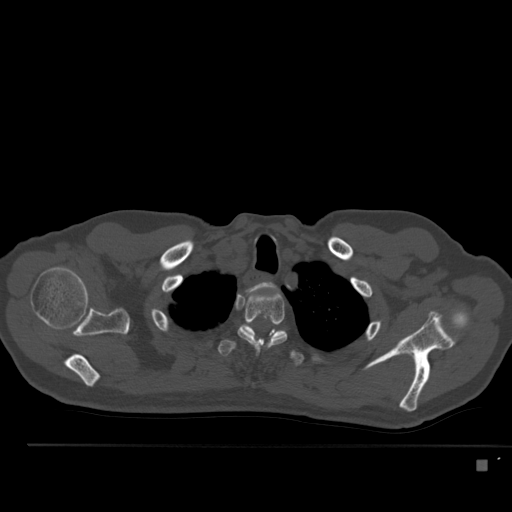
CT including the spine, one axial slice. Position 409 of 517 along the scan axis. Reconstruction kernel Br40s. Bone window (W 1800 / L 400 HU). 512 × 512 image matrix. Male patient, age 70 years. From the clinical record (not read from this slice): primary cancer: renal; vertebrae with lytic lesions (as recorded): T4, T6, T10, T12, L3, L4, L5.
Structures marked on this image (semi-automatically segmented with operator editing):
- T1 vertebra: box from (x=250, y=285) to (x=259, y=291) px
- T2 vertebra: (x=237, y=291)–(x=288, y=350)
- T3 vertebra: (x=217, y=323)–(x=304, y=366)